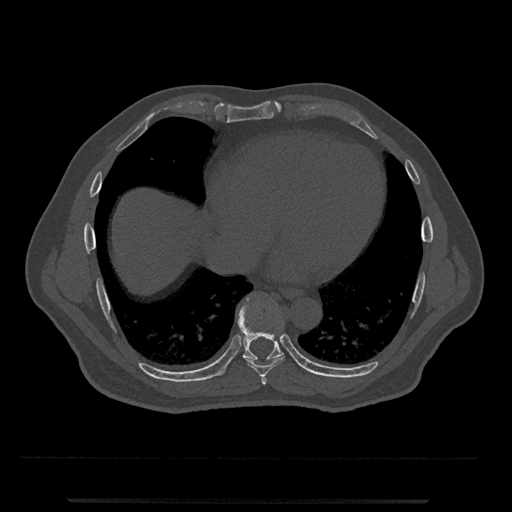
CT including the spine, one axial slice; slice 602 of 797 in the series (ordered by position); reconstruction kernel Br40s/3; bone window (W 1800 / L 400 HU); 512 × 512 image matrix, field of view 419 × 419 mm. Male patient, age 63 years. From the clinical record (not read from this slice): primary cancer: prostate.
Structures marked on this image (semi-automatic segmentation, software-assisted and operator-edited):
- T7 vertebra: bounding box <261,376,267,385> (left, top, right, bottom; pixels)
- T8 vertebra: <244,335,285,377>
- T9 vertebra: <221,297,284,374>